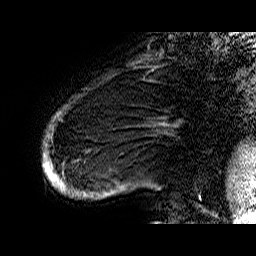
Breast MRI (dynamic contrast-enhanced), one sagittal slice; slice 7 of 60 in the series (ordered by position); dynamic contrast-enhanced series, time point 2 of 6 at this slice position (early post-contrast); 1.5 T; TE 6.4 ms, TR 32.9 ms; 256 × 256 image matrix, field of view 200 × 200 mm. Female patient. Case-level facts recorded for this patient, not image findings: setting: breast cancer imaged before/during neoadjuvant chemotherapy; receptor status: HR-positive, HER2-negative.
Structures marked on this image (semi-automatic segmentation, software-assisted and operator-edited):
- analysis volume of interest (the breast-tissue region the enhancement analysis was run in; not a lesion): bounding box (x1, y1, x2, y2) in pixels: (42, 79, 172, 207)
- tumour enhancement mask (voxels above the 100 % enhancement threshold inside the analysis volume of interest): (43, 154, 64, 192)